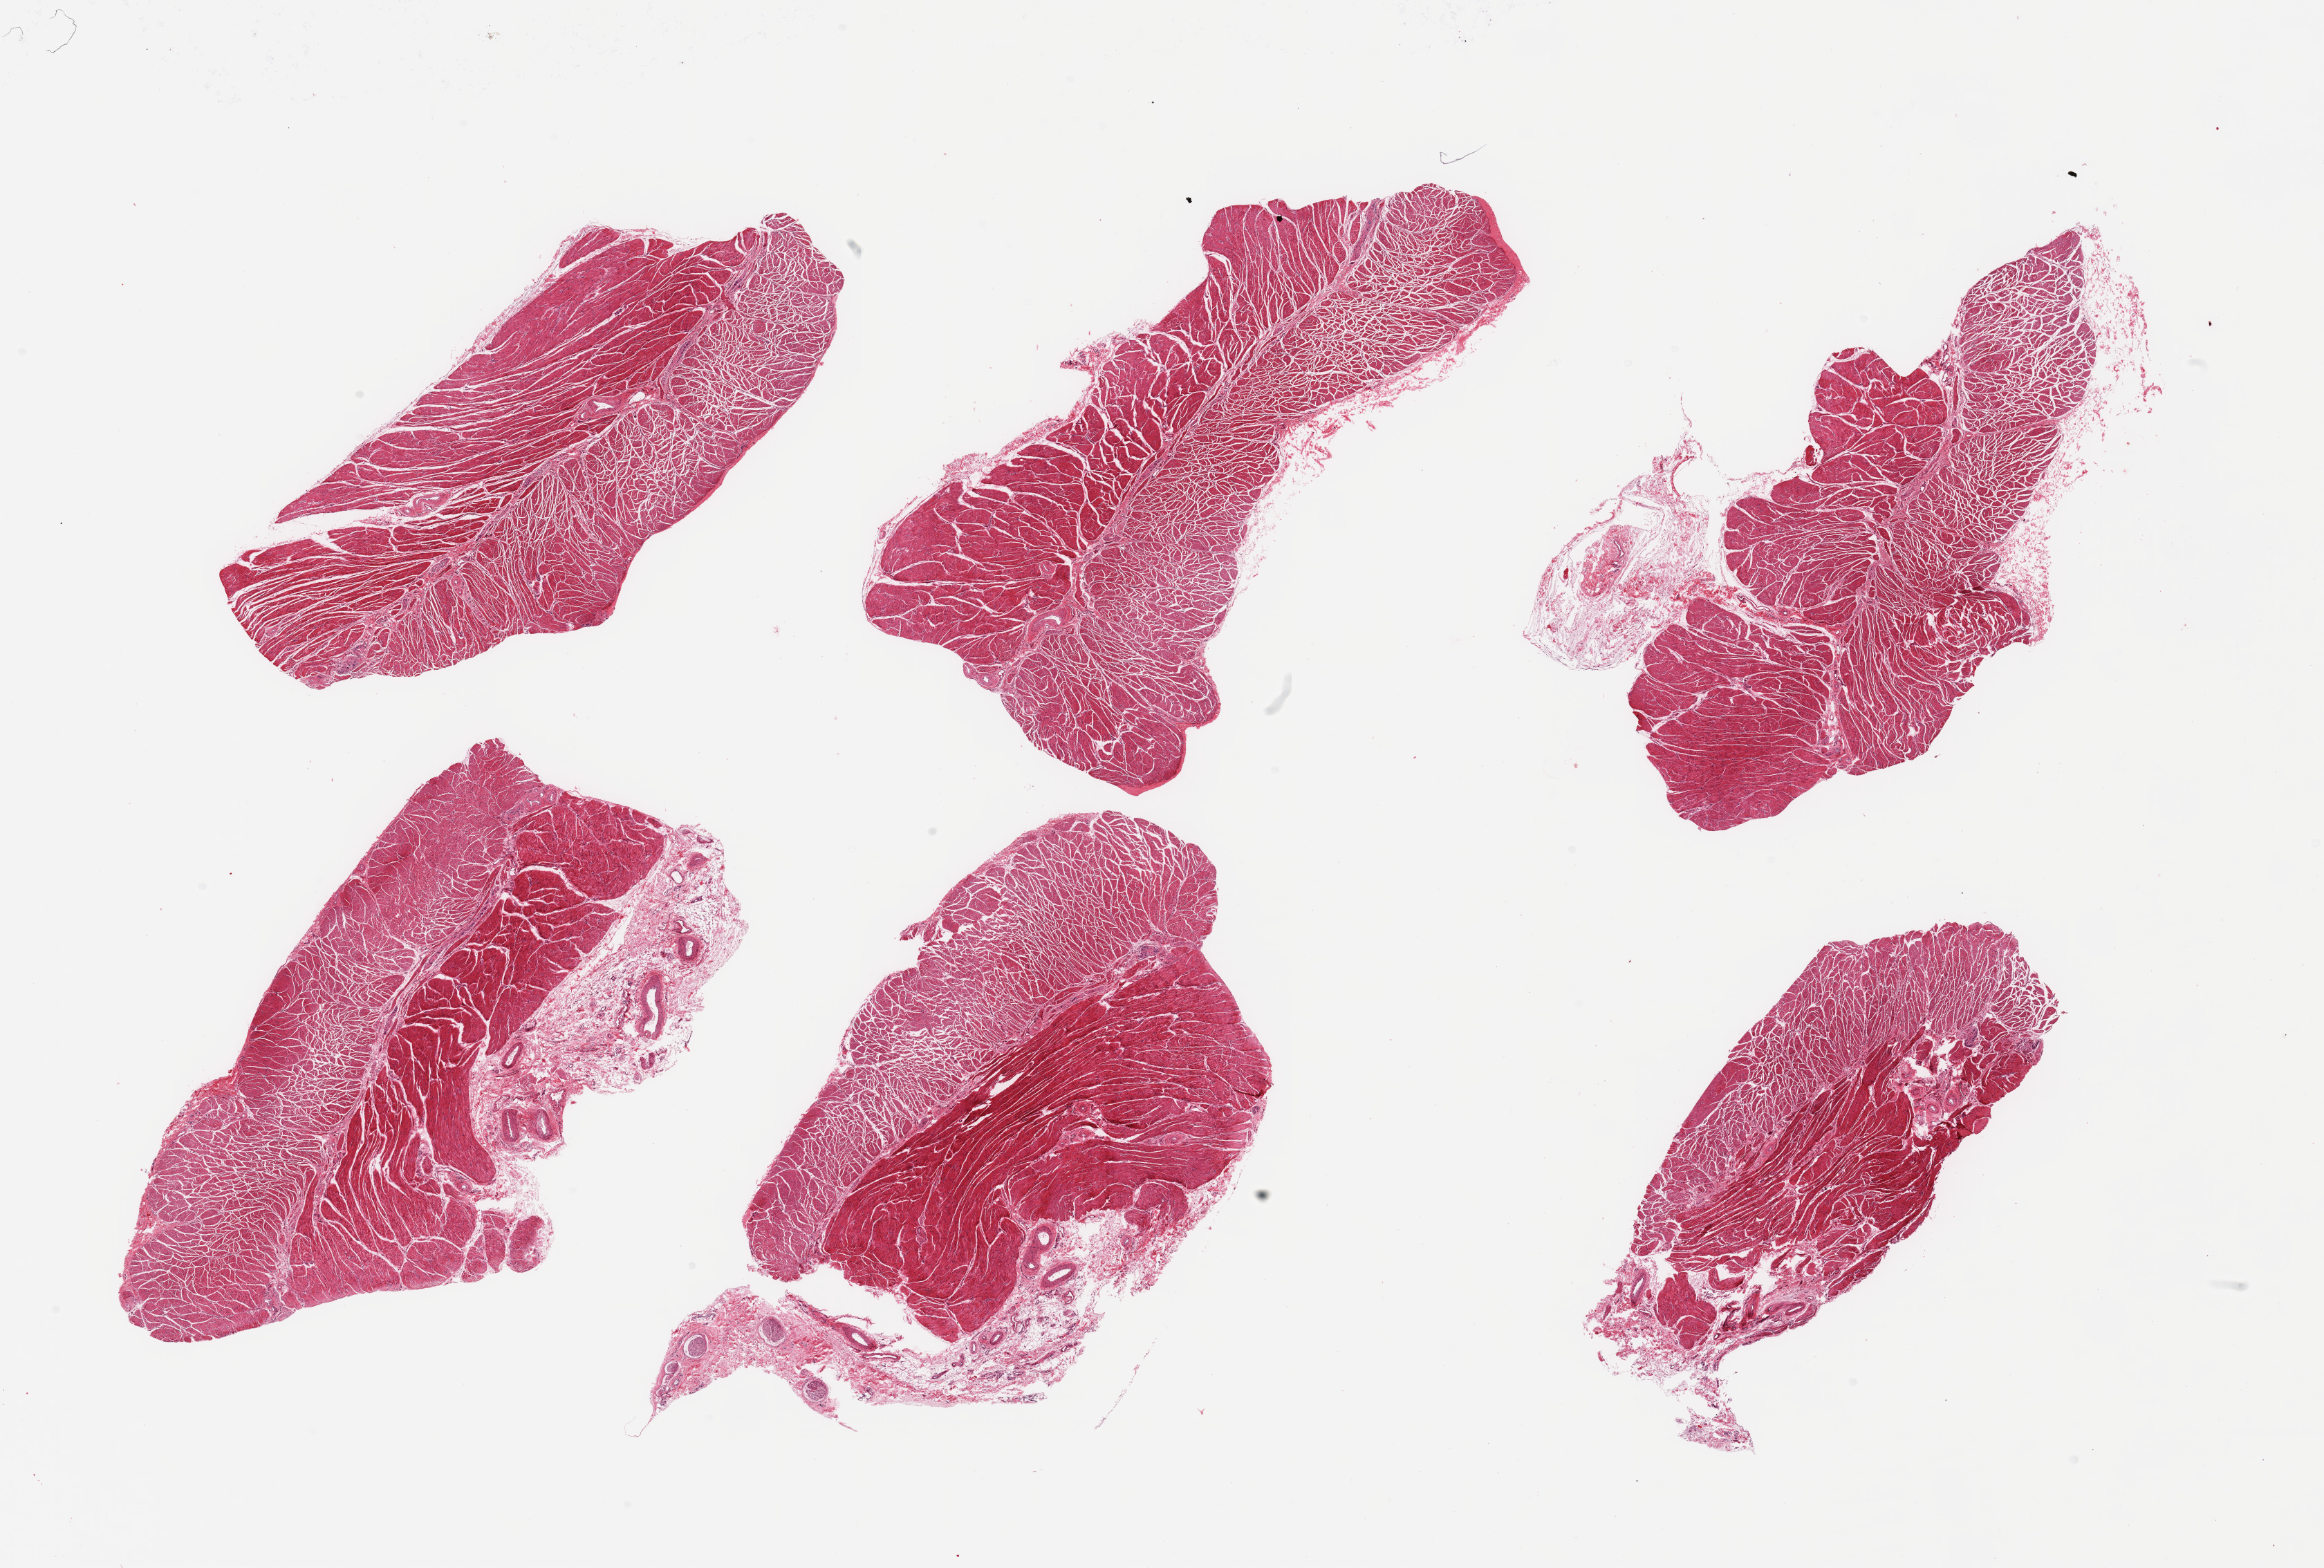
Digitized H&E-stained section, whole scanned area (about 26.6 x 17.9 mm) shown as a low-resolution overview; PAXgene-fixed, paraffin-embedded tissue; sampled site (target tissue): esophageal muscle; donor tissue sample. Donor sex: female.
- reviewer comment on this tissue sample: 6 pieces, confirmed target muscularis, nubbins of adherent fat/fascia up to ~1.5mm